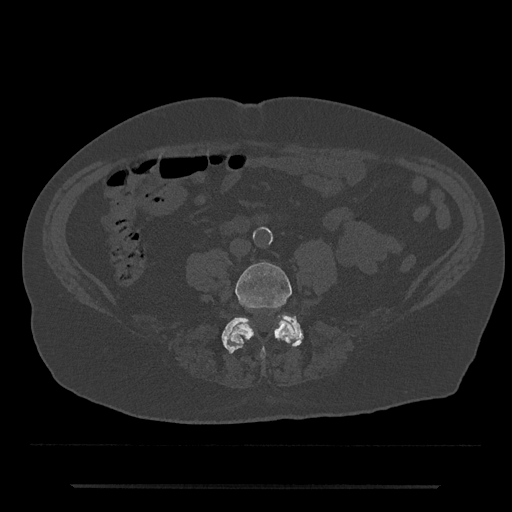
CT including the spine, one axial slice. Position 329 of 797 along the scan axis. Reconstruction kernel Br40s/3. 120 kVp. Bone window (W 1800 / L 400 HU). 0.5 mm slice thickness. 512 × 512 image matrix, field of view 434 × 434 mm. Male patient, age 80 years. Case-level facts recorded for this patient, not image findings: primary cancer: prostate.
Outlined on this slice (semi-automatic segmentation, software-assisted and operator-edited):
- L4 vertebra: bounding box [x1, y1, x2, y2] px = [228, 262, 297, 359]
- L5 vertebra: [222, 315, 303, 353]